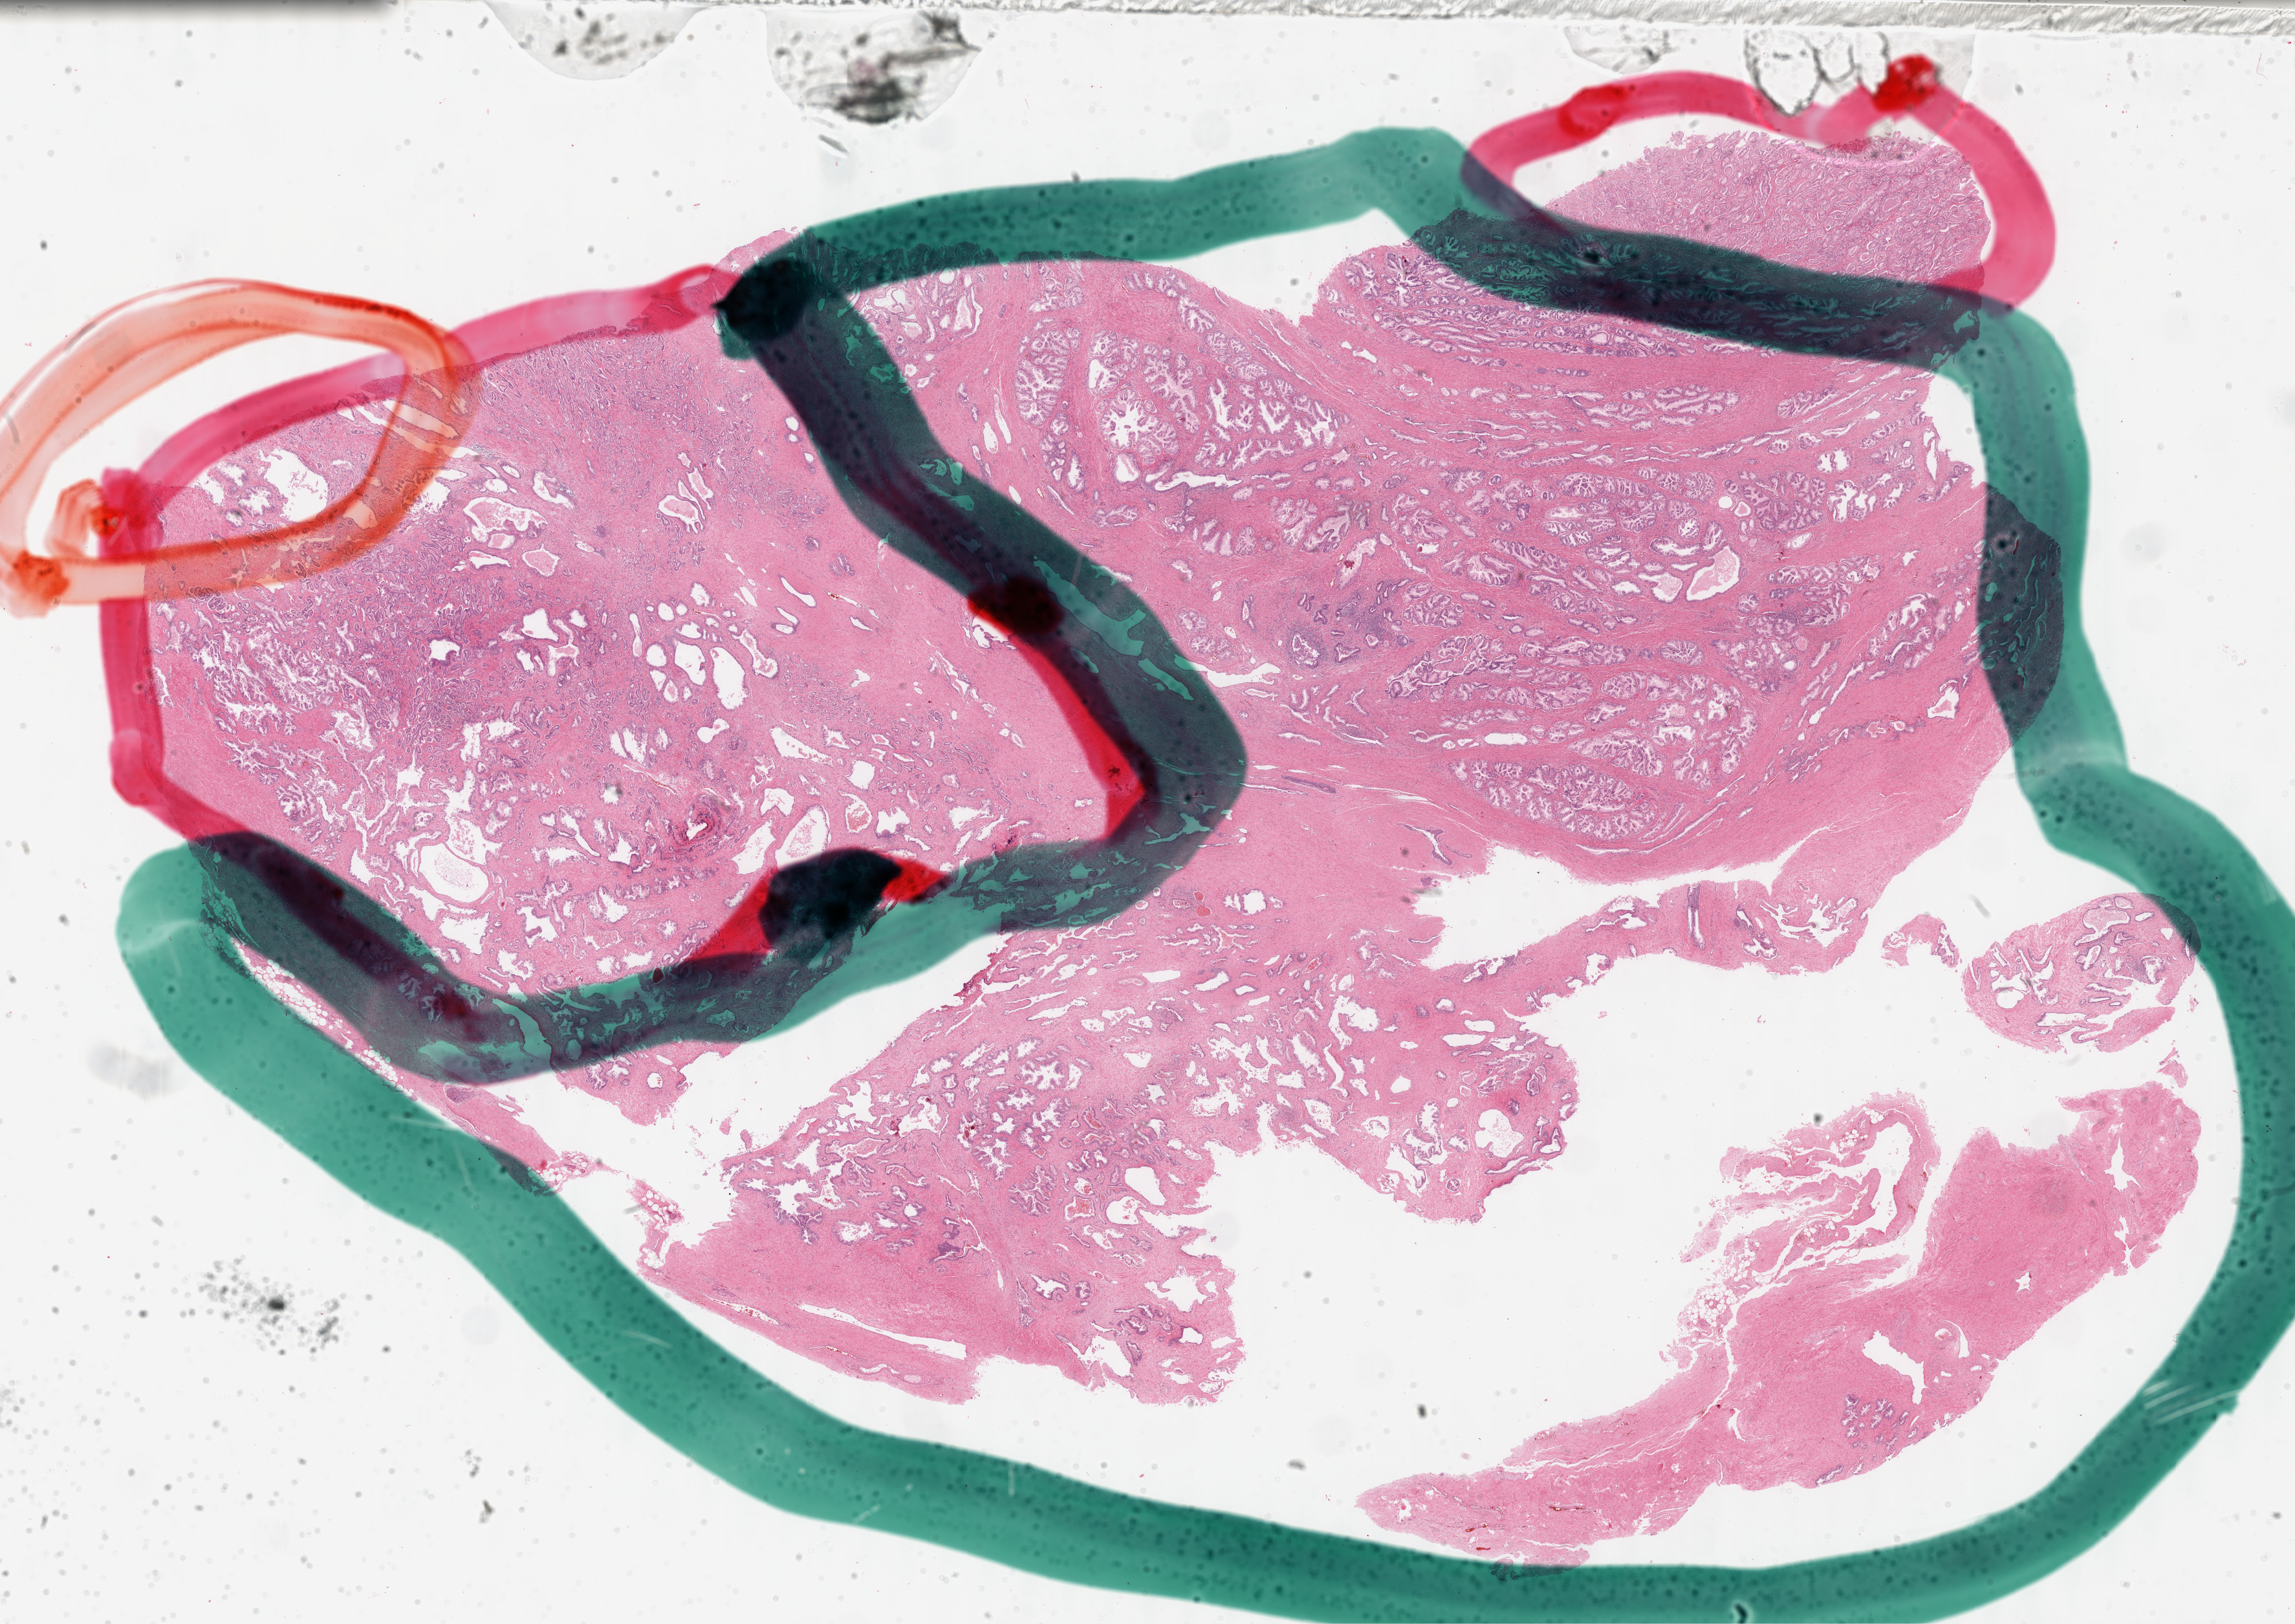
Digitized H&E tissue section (whole slide), shown as a low-resolution overview of the whole scanned area (about 28.7 x 20.3 mm, from a 40x scan); formalin-fixed paraffin-embedded (FFPE) diagnostic section; primary tumour sample from the prostate. Male, age 68 years at initial diagnosis. Gleason score: 6 (3+3).
• pathologic diagnosis: Adenocarcinoma, NOS (prostate gland)